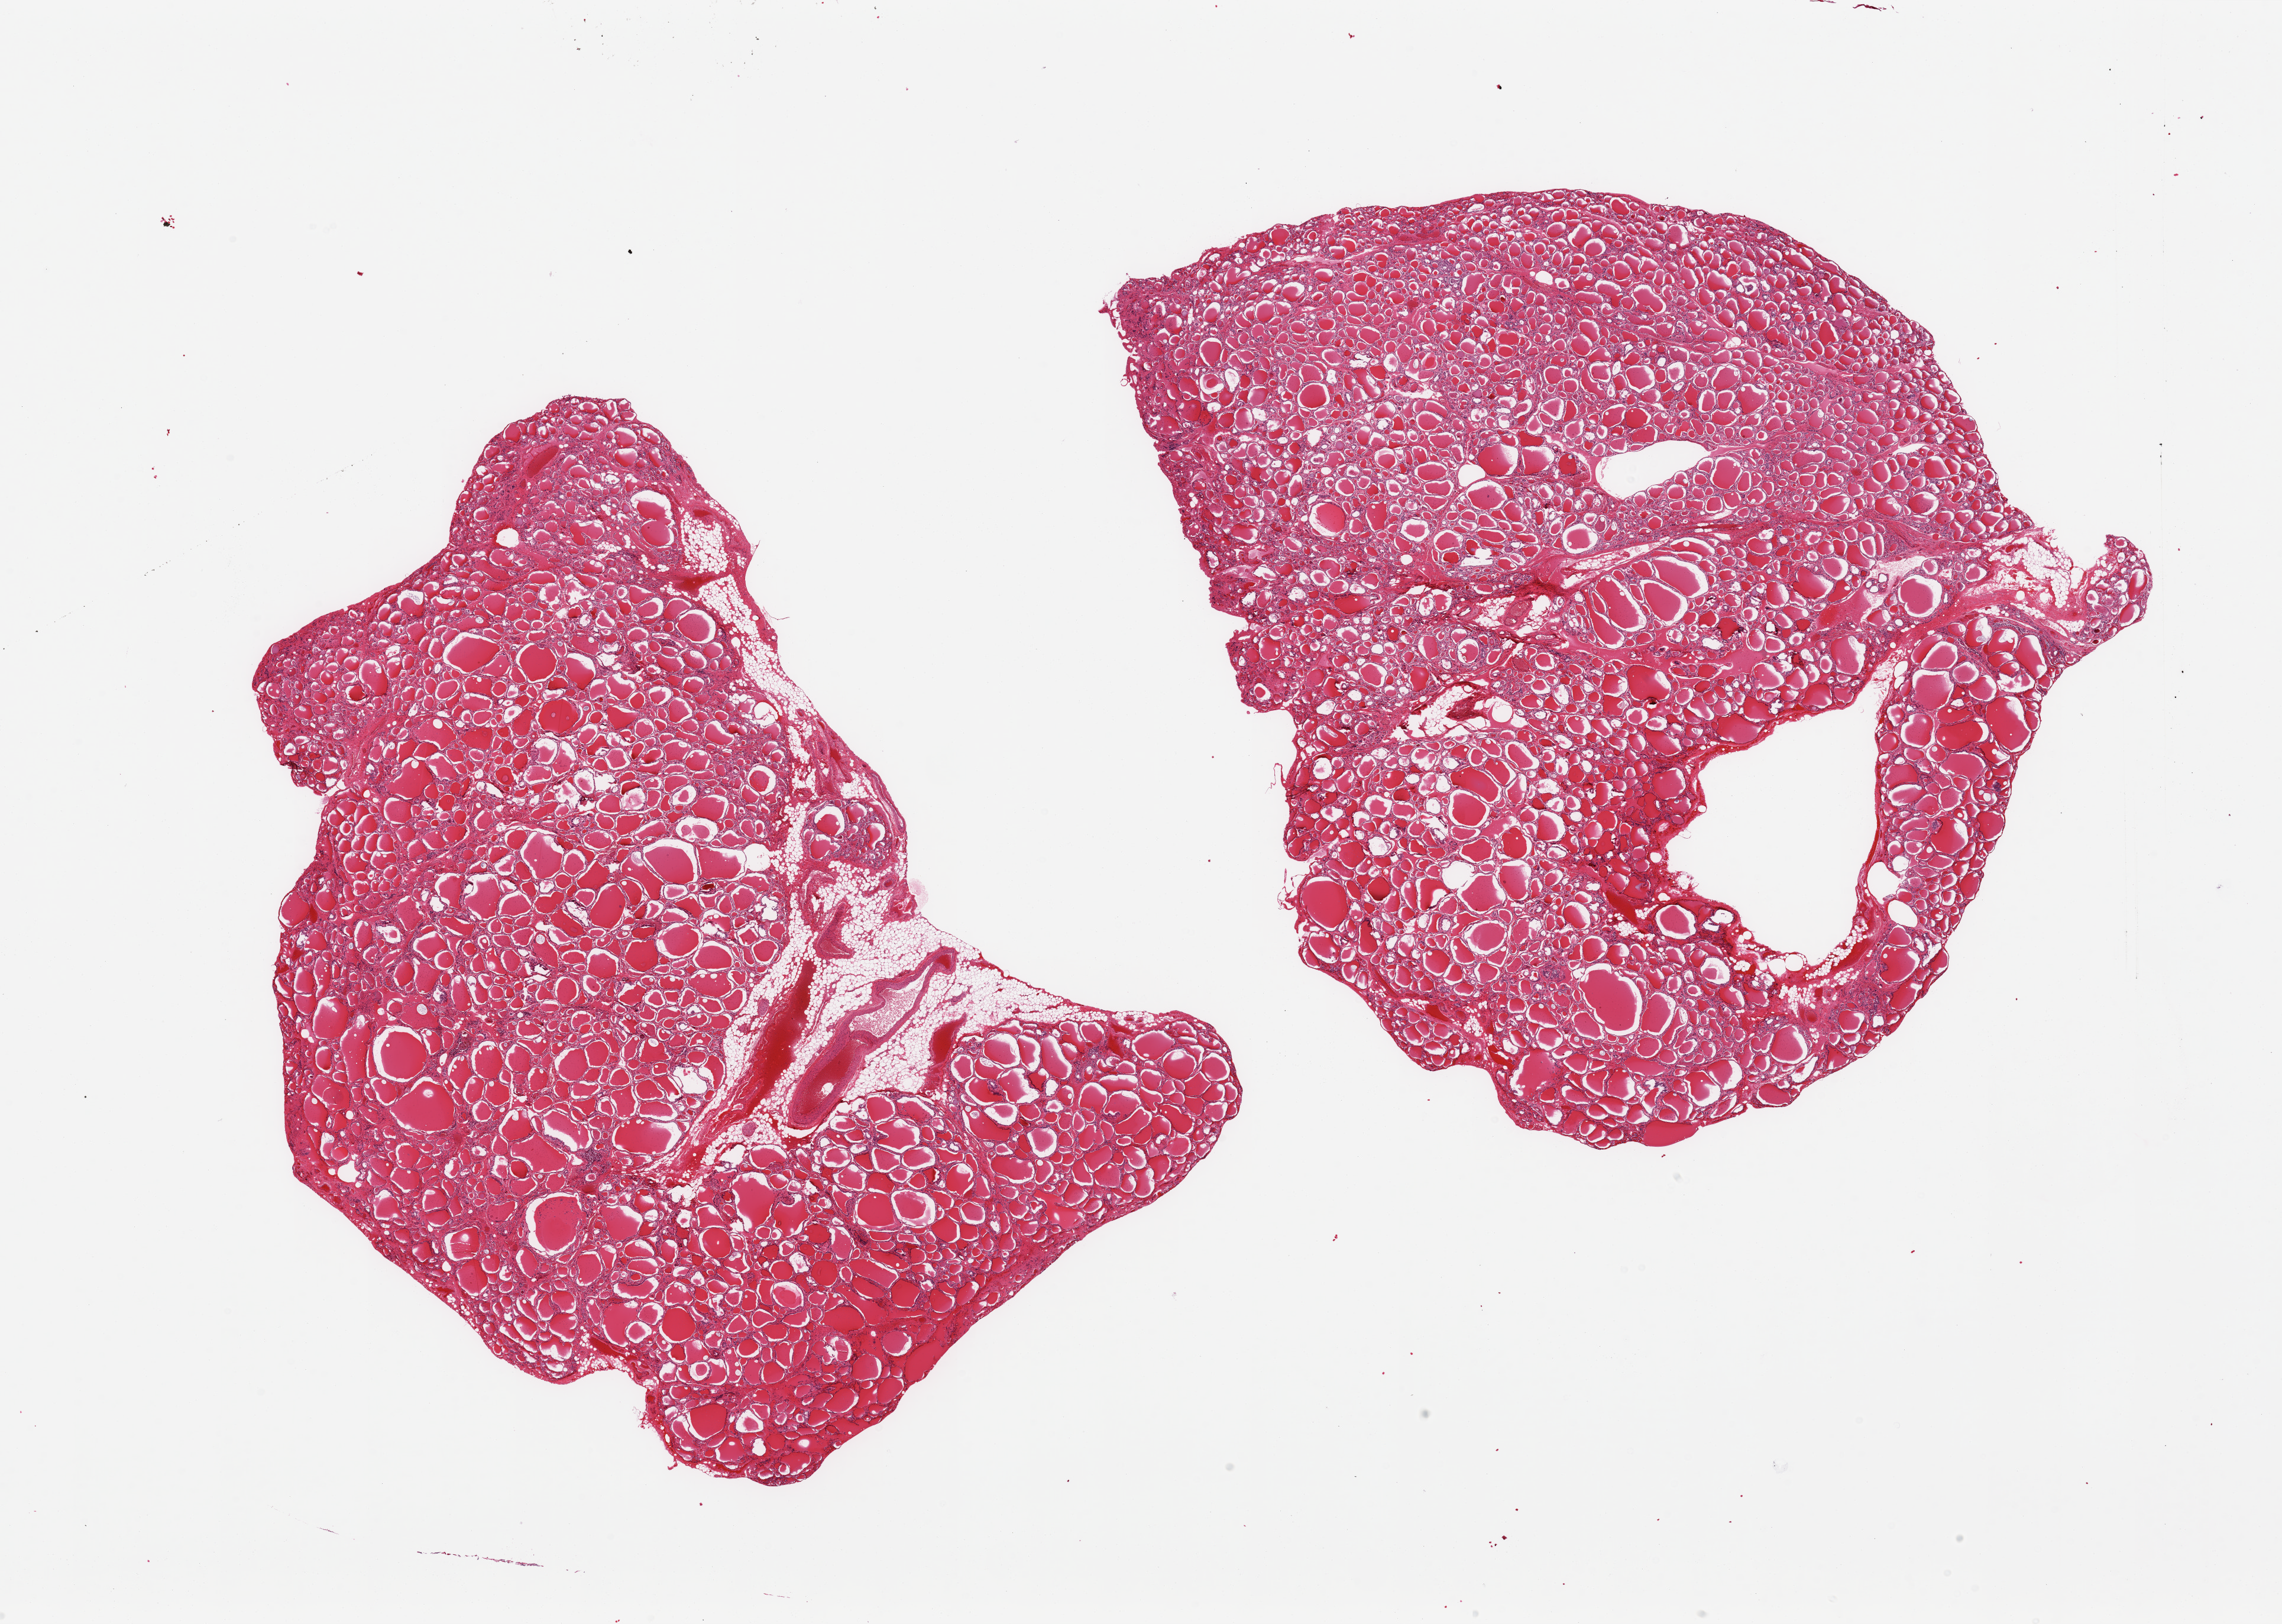
Hematoxylin and eosin (H&E) whole-slide image, shown as a low-resolution overview of the whole scanned area (about 30.5 x 21.7 mm), PAXgene-fixed paraffin-embedded (PFPE) section, target tissue: thyroid, tissue donor sample. Donor sex: male.
Review note (as recorded): 2 pieces; 15% and 5% fat mostly perivascular; couple of empty spaces.